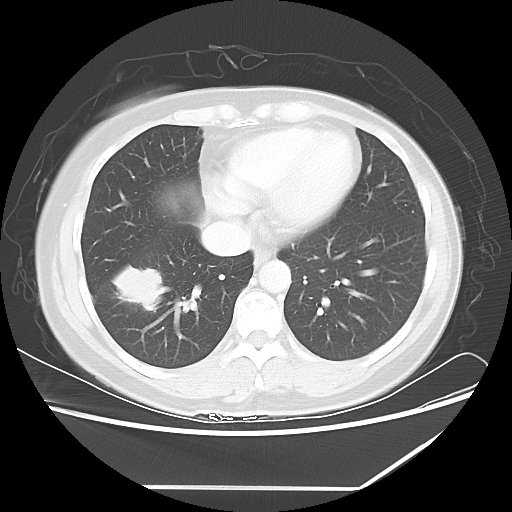
Chest CT, one axial slice. Position 22 of 60 along the scan axis. Reconstruction kernel LUNG. Lung window (W 1500 / L -600 HU). 5 mm slice thickness. 512 × 512 image matrix, field of view 374 × 374 mm. Patient: female, 42 years. From the clinical record (not read from this slice): clinical TNM (as recorded): T2 N1 M0.
Outlined on this slice (bounding box drawn by a radiologist):
- lung tumour (recorded histology: adenocarcinoma): box from (x=108, y=258) to (x=167, y=312) px